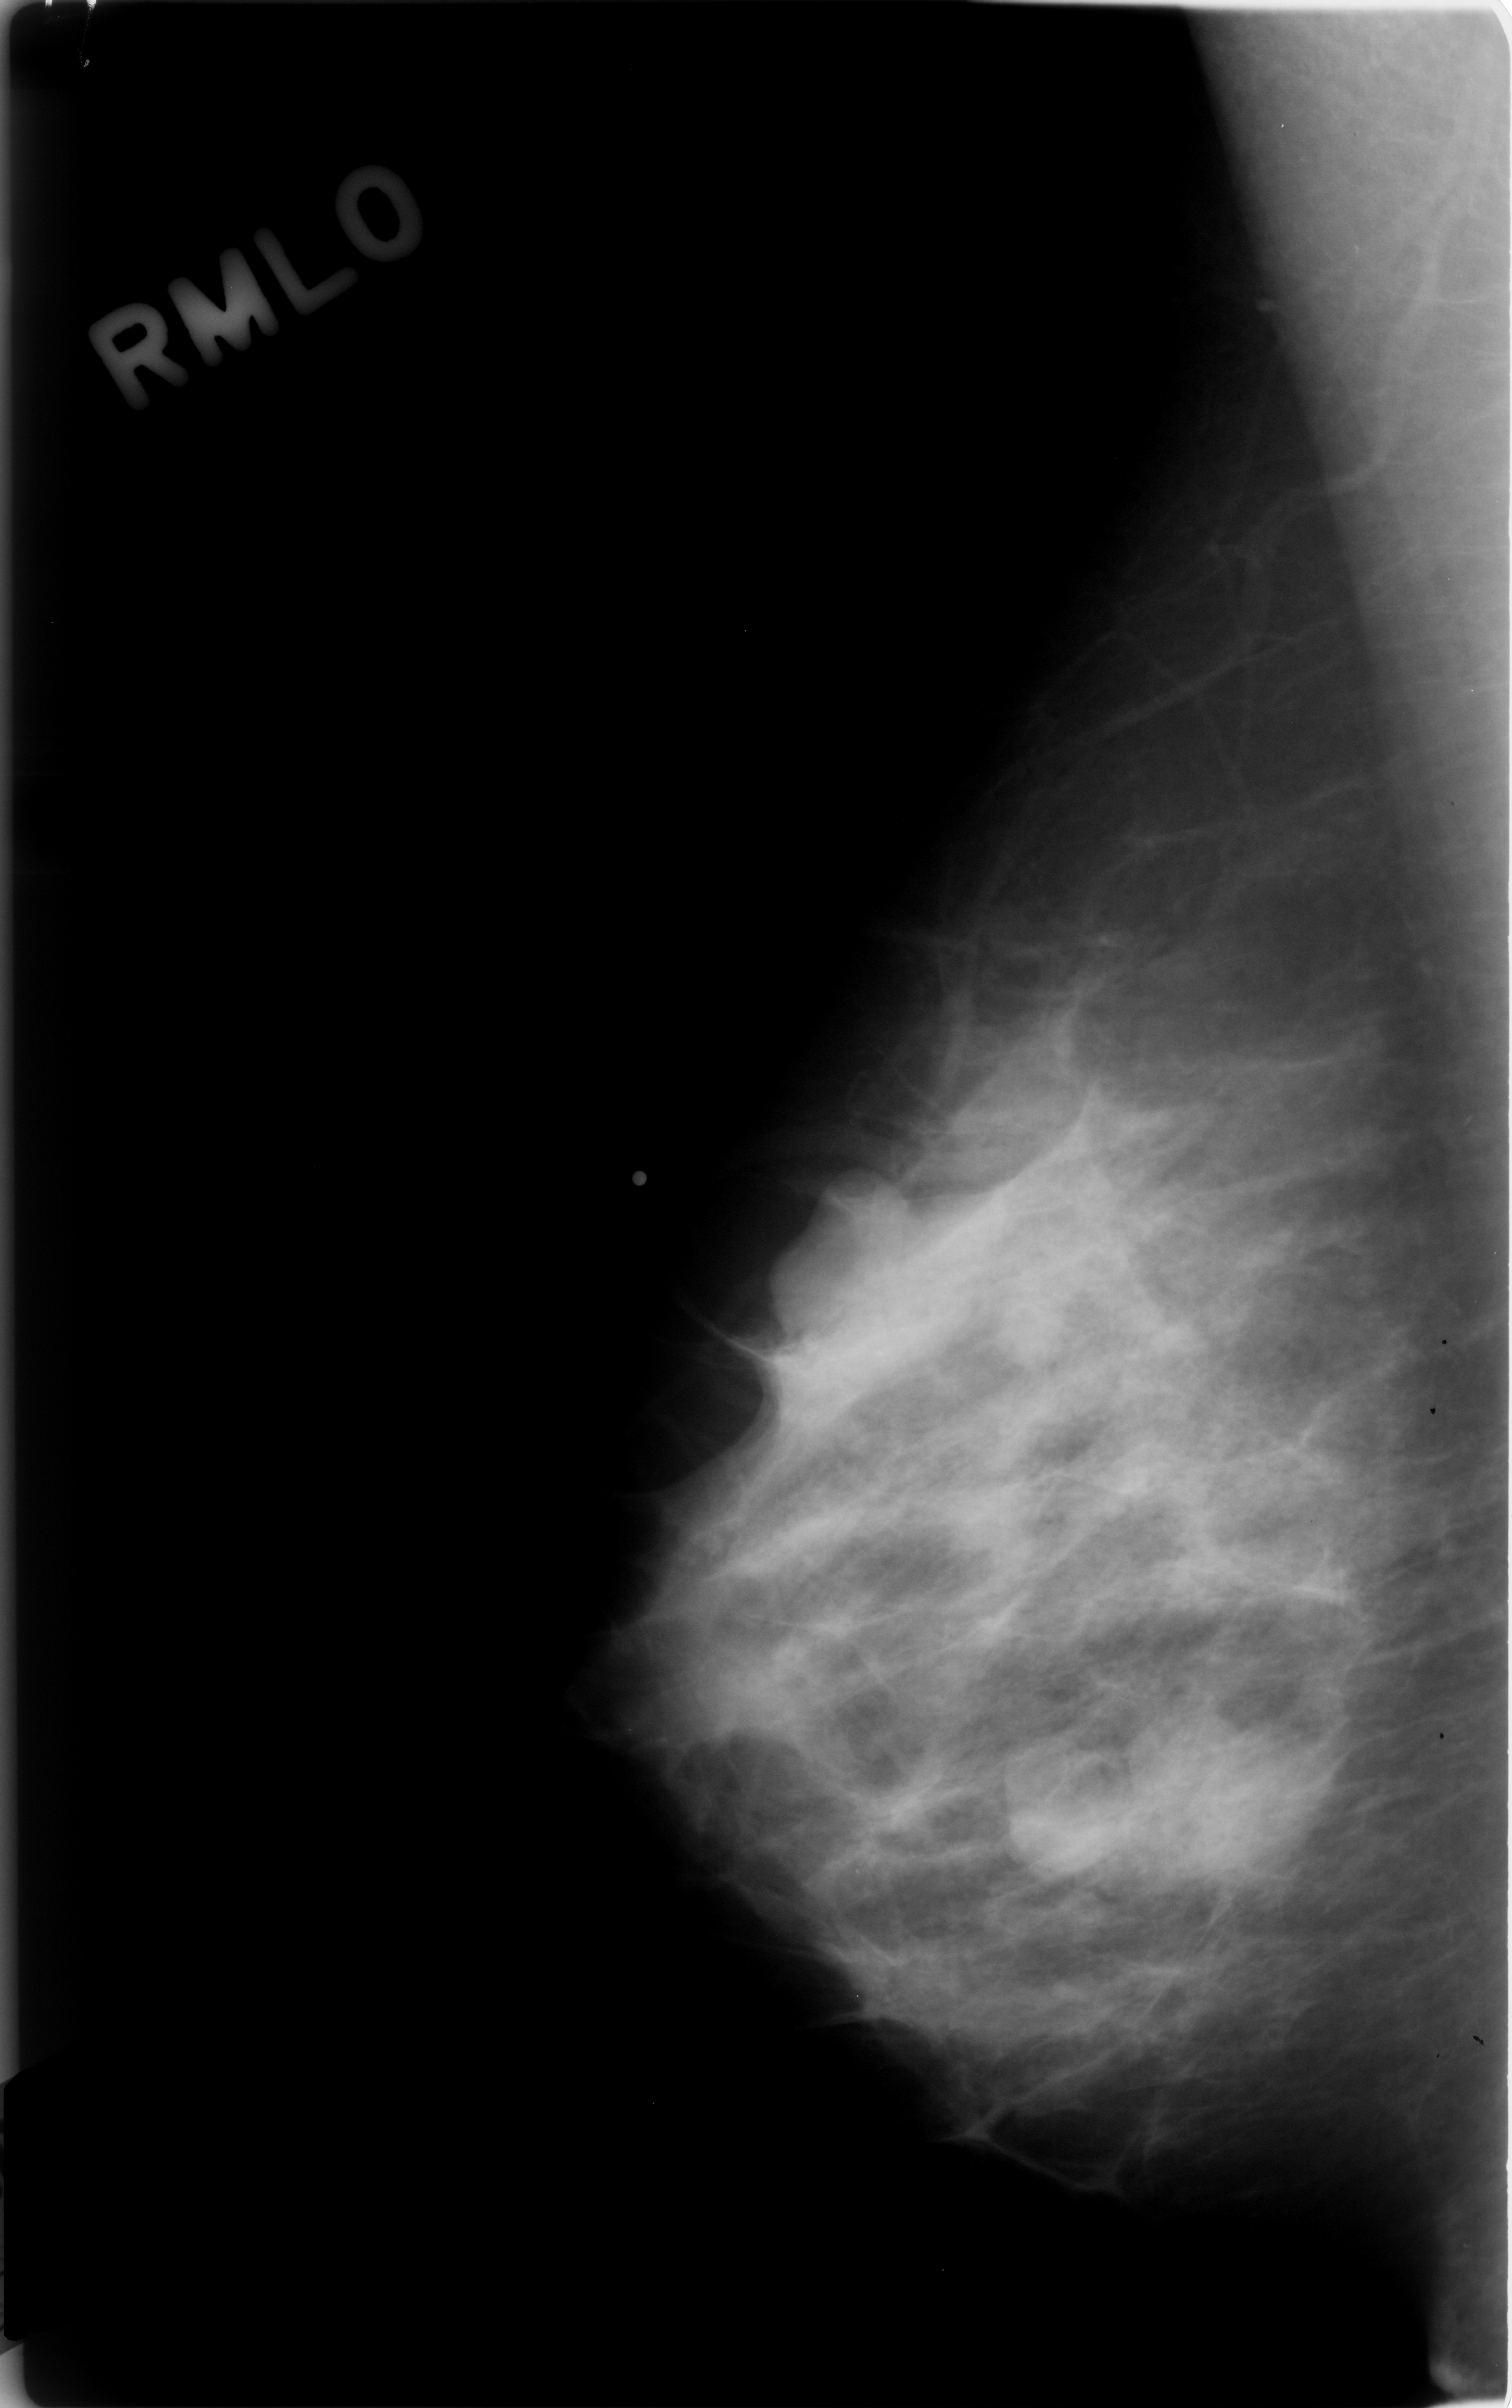
Digitized screen-film mammogram; right breast; mediolateral oblique (MLO) view; 1512 × 2408 image matrix.
Expert-marked regions of interest on this film, with their recorded descriptors:
- mass, shape lobulated, margins obscured; BI-RADS assessment category 4; subtlety rating 5 on a 1 (subtle) to 5 (obvious) scale; pathology result (as recorded, not read from the image): benign: box from (x=1009, y=1686) to (x=1332, y=1922) px